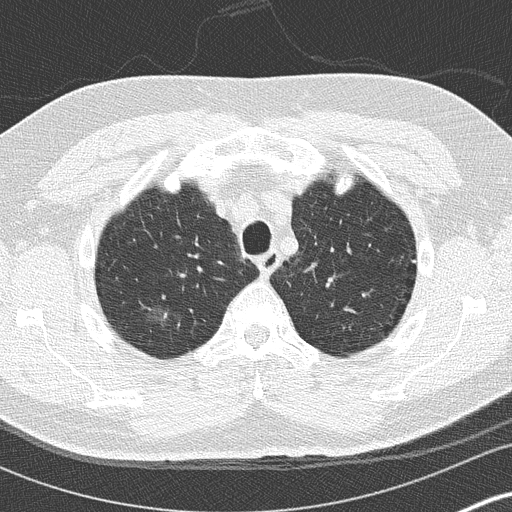
Low-dose screening chest CT, axial slice; baseline annual screen; lung window (W 1500 / L -600 HU); 2 mm slice thickness; 120 kVp. Male, age 59 years at enrolment. Current smoker at enrolment.
- Expert reader's lesion annotation, bounding box [x1, y1, x2, y2] px = [141, 294, 191, 343].
- The exam's reader record, not a measurement of the box and not confirmed to be the same lesion: non-calcified nodule or mass ≥4 mm, right upper lobe, 16 × 16 mm, ground glass attenuation.
- Official screen result: positive, change unspecified: nodule(s) >= 4 mm or enlarging nodule(s), mass(es), or other non-specific abnormalities suspicious for lung cancer.